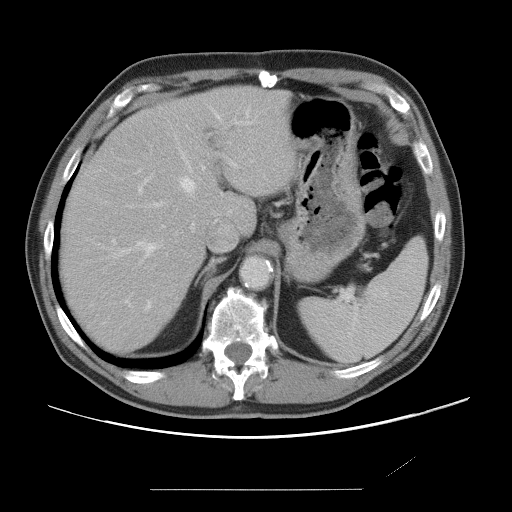
Contrast-enhanced abdominal CT, one axial slice; position 53 of 87 along the scan axis; 120 kVp; intravenous contrast given; soft-tissue window (W 400 / L 40 HU); 5 mm slice thickness; 512 × 512 image matrix, field of view 406 × 406 mm. Male patient, age 74 years. Case-level facts recorded for this patient, not image findings: diagnosis: colorectal cancer liver metastases, imaged before liver resection; multiple liver metastases: yes; largest metastasis: 1.1 cm; disease in both lobes: no.
Outlined on this slice (manually delineated by an expert):
- hepatic veins: bounding box (x1, y1, x2, y2) in pixels: (121, 110, 251, 309)
- liver: (61, 88, 295, 352)
- planned liver remnant (the part of the liver to remain after resection): (61, 88, 295, 352)
- portal vein (with intrahepatic branches): (112, 160, 238, 305)